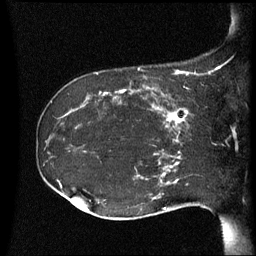
Breast MRI (dynamic contrast-enhanced), one sagittal slice; slice 23 of 60 in the series (ordered by position); dynamic contrast-enhanced series, image 2 of 3 at this slice position (ordered by acquisition); 1.5 T; TE 4.2 ms, TR 8.4 ms; 2.5 mm slice thickness; 256 × 256 image matrix, field of view 220 × 220 mm. Female patient, age 41 years. From the clinical record (not read from this slice): setting: breast cancer imaged before/during neoadjuvant chemotherapy; receptor status: HER2-positive.
Outlined on this slice (semi-automatically segmented with operator editing):
- analysis volume of interest (the breast-tissue region the enhancement analysis was run in; not a lesion): box from (x=122, y=84) to (x=195, y=137) px
- tumour enhancement mask (voxels above the 70 % enhancement threshold inside the analysis volume of interest): (x=122, y=86)–(x=192, y=137)